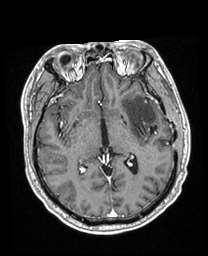
Brain MRI from a brain-tumour surgery series, one axial slice. Slice 111 of 208 in the series (ordered by position). T1-weighted post-contrast. 208 × 256 image matrix, field of view 211 × 260 mm. From the clinical record (not read from this slice): histopathology: Astrocytoma; WHO grade: 3; IDH mutation: yes.
Outlined on this slice (manually delineated by an expert):
- previous resection cavity: bounding box (x1, y1, x2, y2) in pixels: (150, 126, 157, 135)